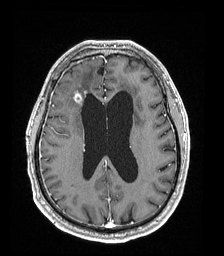
Brain MRI from a brain-tumour surgery series, one axial slice; slice 76 of 192 in the series (ordered by position); T1-weighted post-contrast; 1 mm slice thickness; 224 × 256 image matrix, field of view 224 × 256 mm. Case-level facts recorded for this patient, not image findings: histopathology: Astrocytoma; WHO grade: 4; IDH mutation: yes; tumour location: Right Frontal.
Annotated regions visible in this slice (expert manual segmentation):
- tumour: bounding box [x1, y1, x2, y2] px = [73, 93, 82, 103]